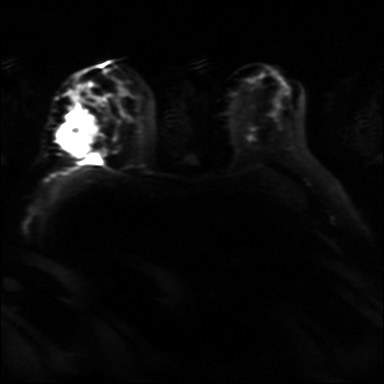
Breast MRI, one axial slice. Slice 21 of 36 in the series (ordered by position). Diffusion-weighted series; image 2 of 4 stored at this slice position (different b-values; order by instance number). 3 T. 4 mm slice thickness. 384 × 384 image matrix, field of view 320 × 320 mm. Female patient.
Annotated regions visible in this slice (outlined manually by an expert reader):
- tumour on diffusion-weighted imaging: box from (x=56, y=114) to (x=97, y=158) px